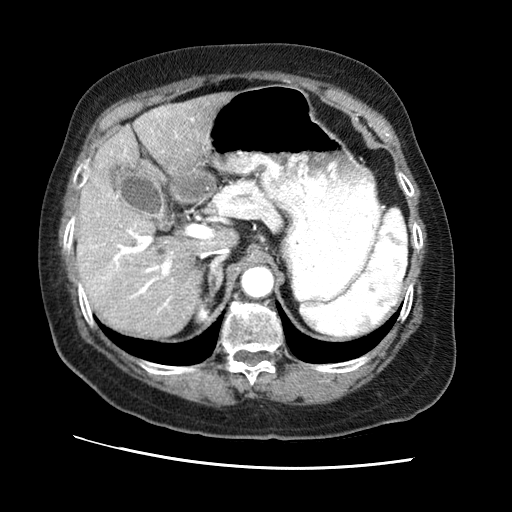
Contrast-enhanced abdominal CT (liver protocol), one axial slice. Position 39 of 65 along the scan axis. Reconstruction kernel STANDARD. 120 kVp. Soft-tissue window (W 400 / L 40 HU). 2.5 mm slice thickness. 512 × 512 image matrix, field of view 340 × 340 mm. From the clinical record (not read from this slice): diagnosis: hepatocellular carcinoma (patient treated with transarterial chemoembolisation; whether this scan precedes or follows treatment is not stated here); TNM stage (as recorded): Stage-II; Child-Pugh class: A; tumour differentiation: no biopsy.
Structures marked on this image (semi-automatically segmented with operator editing):
- liver parenchyma outside the tumour (the mass and vessels are separate outlines, so this box may not span the whole liver): box from (x=76, y=92) to (x=236, y=337) px
- liver vessels: (x=90, y=113)–(x=194, y=312)